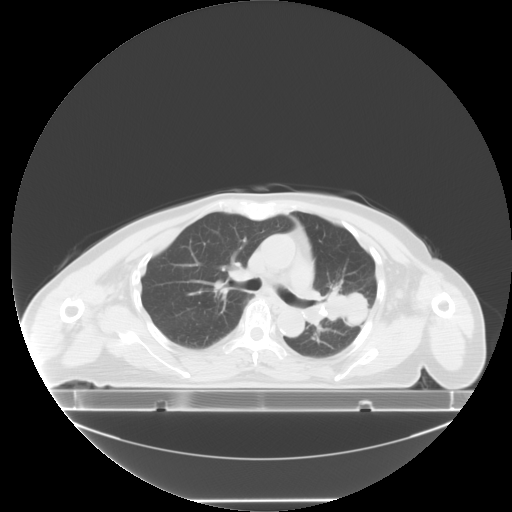
Chest CT, one axial slice; slice 4 of 24 in the series (ordered by position); reconstruction kernel STANDARD; 120 kVp; lung window (W 1500 / L -600 HU); 5 mm slice thickness; 512 × 512 image matrix, field of view 500 × 500 mm. Patient: female, 74 years. From the clinical record (not read from this slice): clinical TNM (as recorded): T3 N1 M1c.
Annotated regions visible in this slice (bounding box drawn by a radiologist):
- lung tumour (recorded histology: small cell carcinoma): bounding box [x1, y1, x2, y2] px = [323, 286, 366, 332]